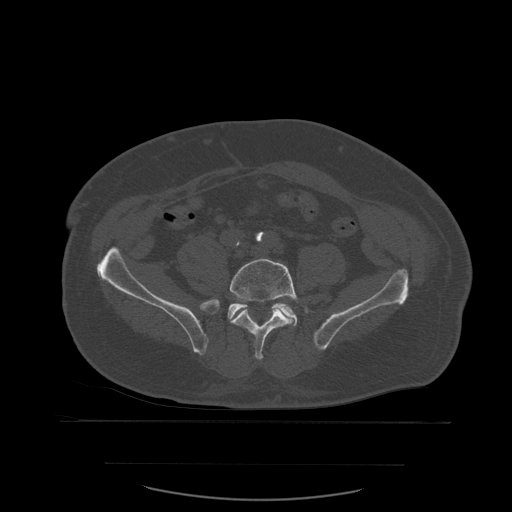
CT including the spine, one axial slice; position 134 of 590 along the scan axis; bone window (W 1800 / L 400 HU); 1.25 mm slice thickness; 512 × 512 image matrix, field of view 479 × 479 mm. Patient age 71 years. Case-level facts recorded for this patient, not image findings: primary cancer: lung; vertebrae with lytic lesions (as recorded): T1, T2, L5, S1.
Structures marked on this image (semi-automatic segmentation, software-assisted and operator-edited):
- L5 vertebra: bounding box (x1, y1, x2, y2) in pixels: (230, 258, 299, 361)